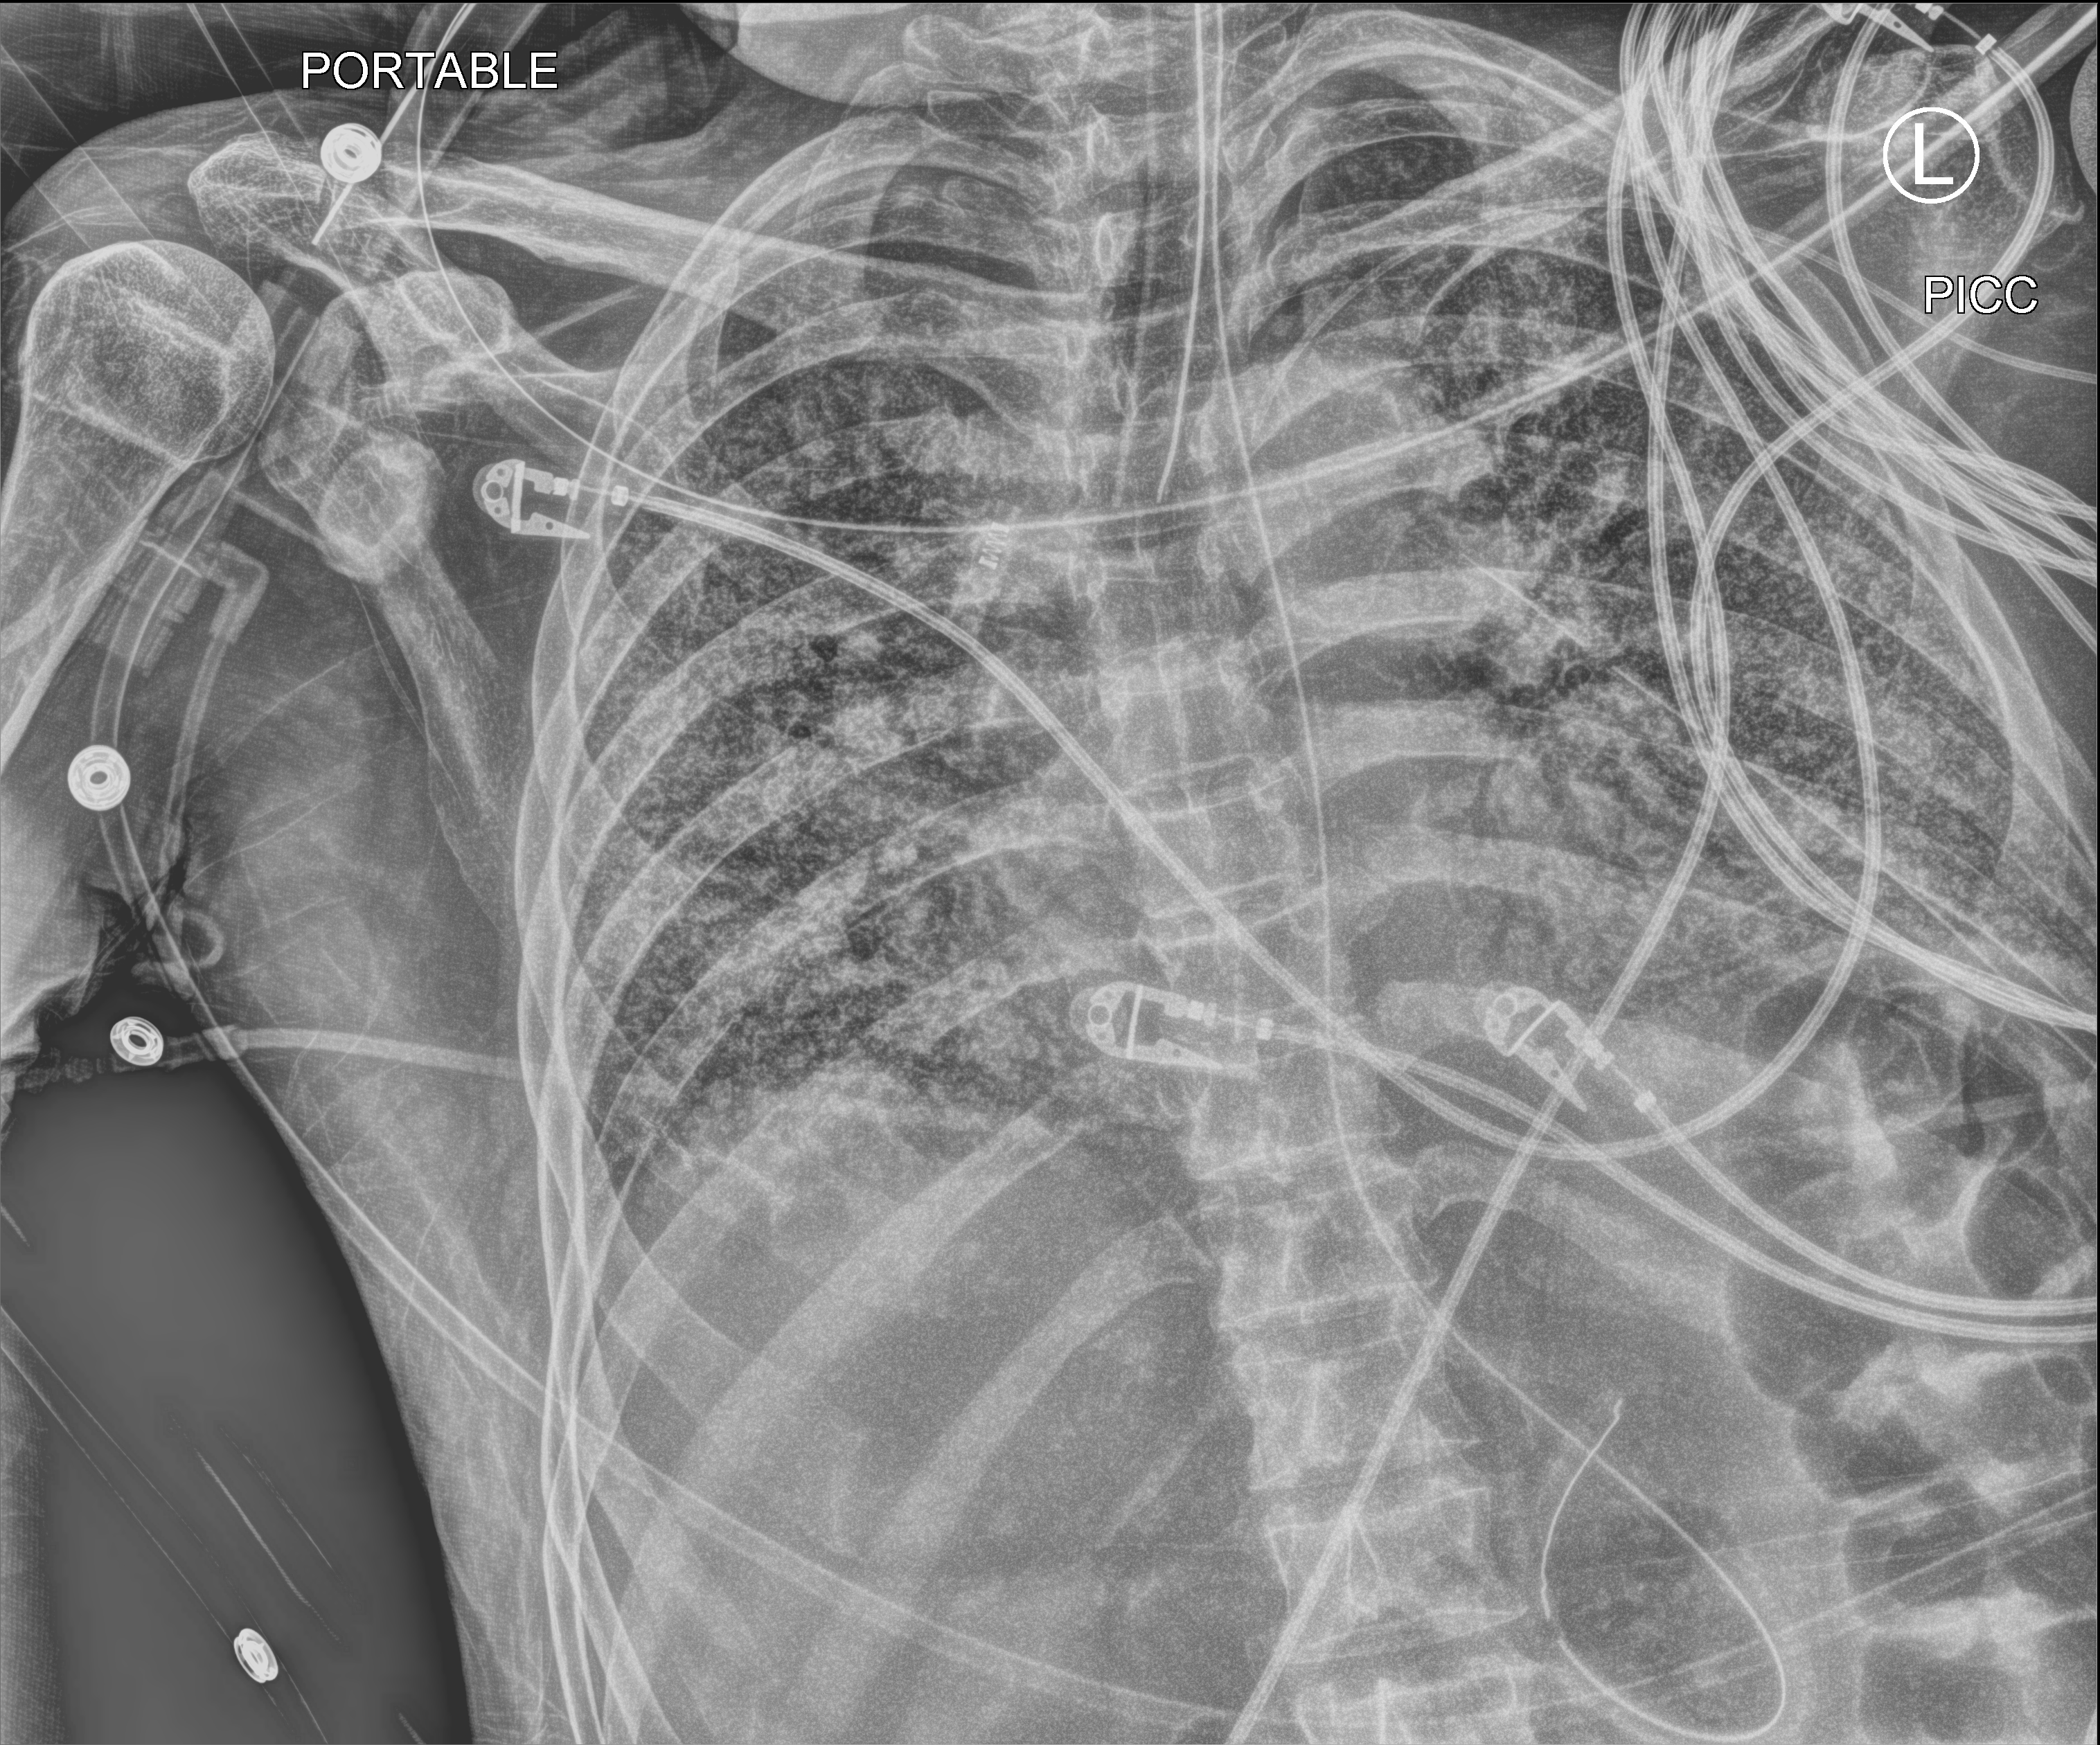
Chest X-ray (portable), anteroposterior (AP) projection. Patient hospitalised with COVID-19; male, aged 60–74 years.
Admission-level facts for this patient (not findings on this image; timing relative to this image not recorded): admitted to intensive care during this hospital stay: yes.